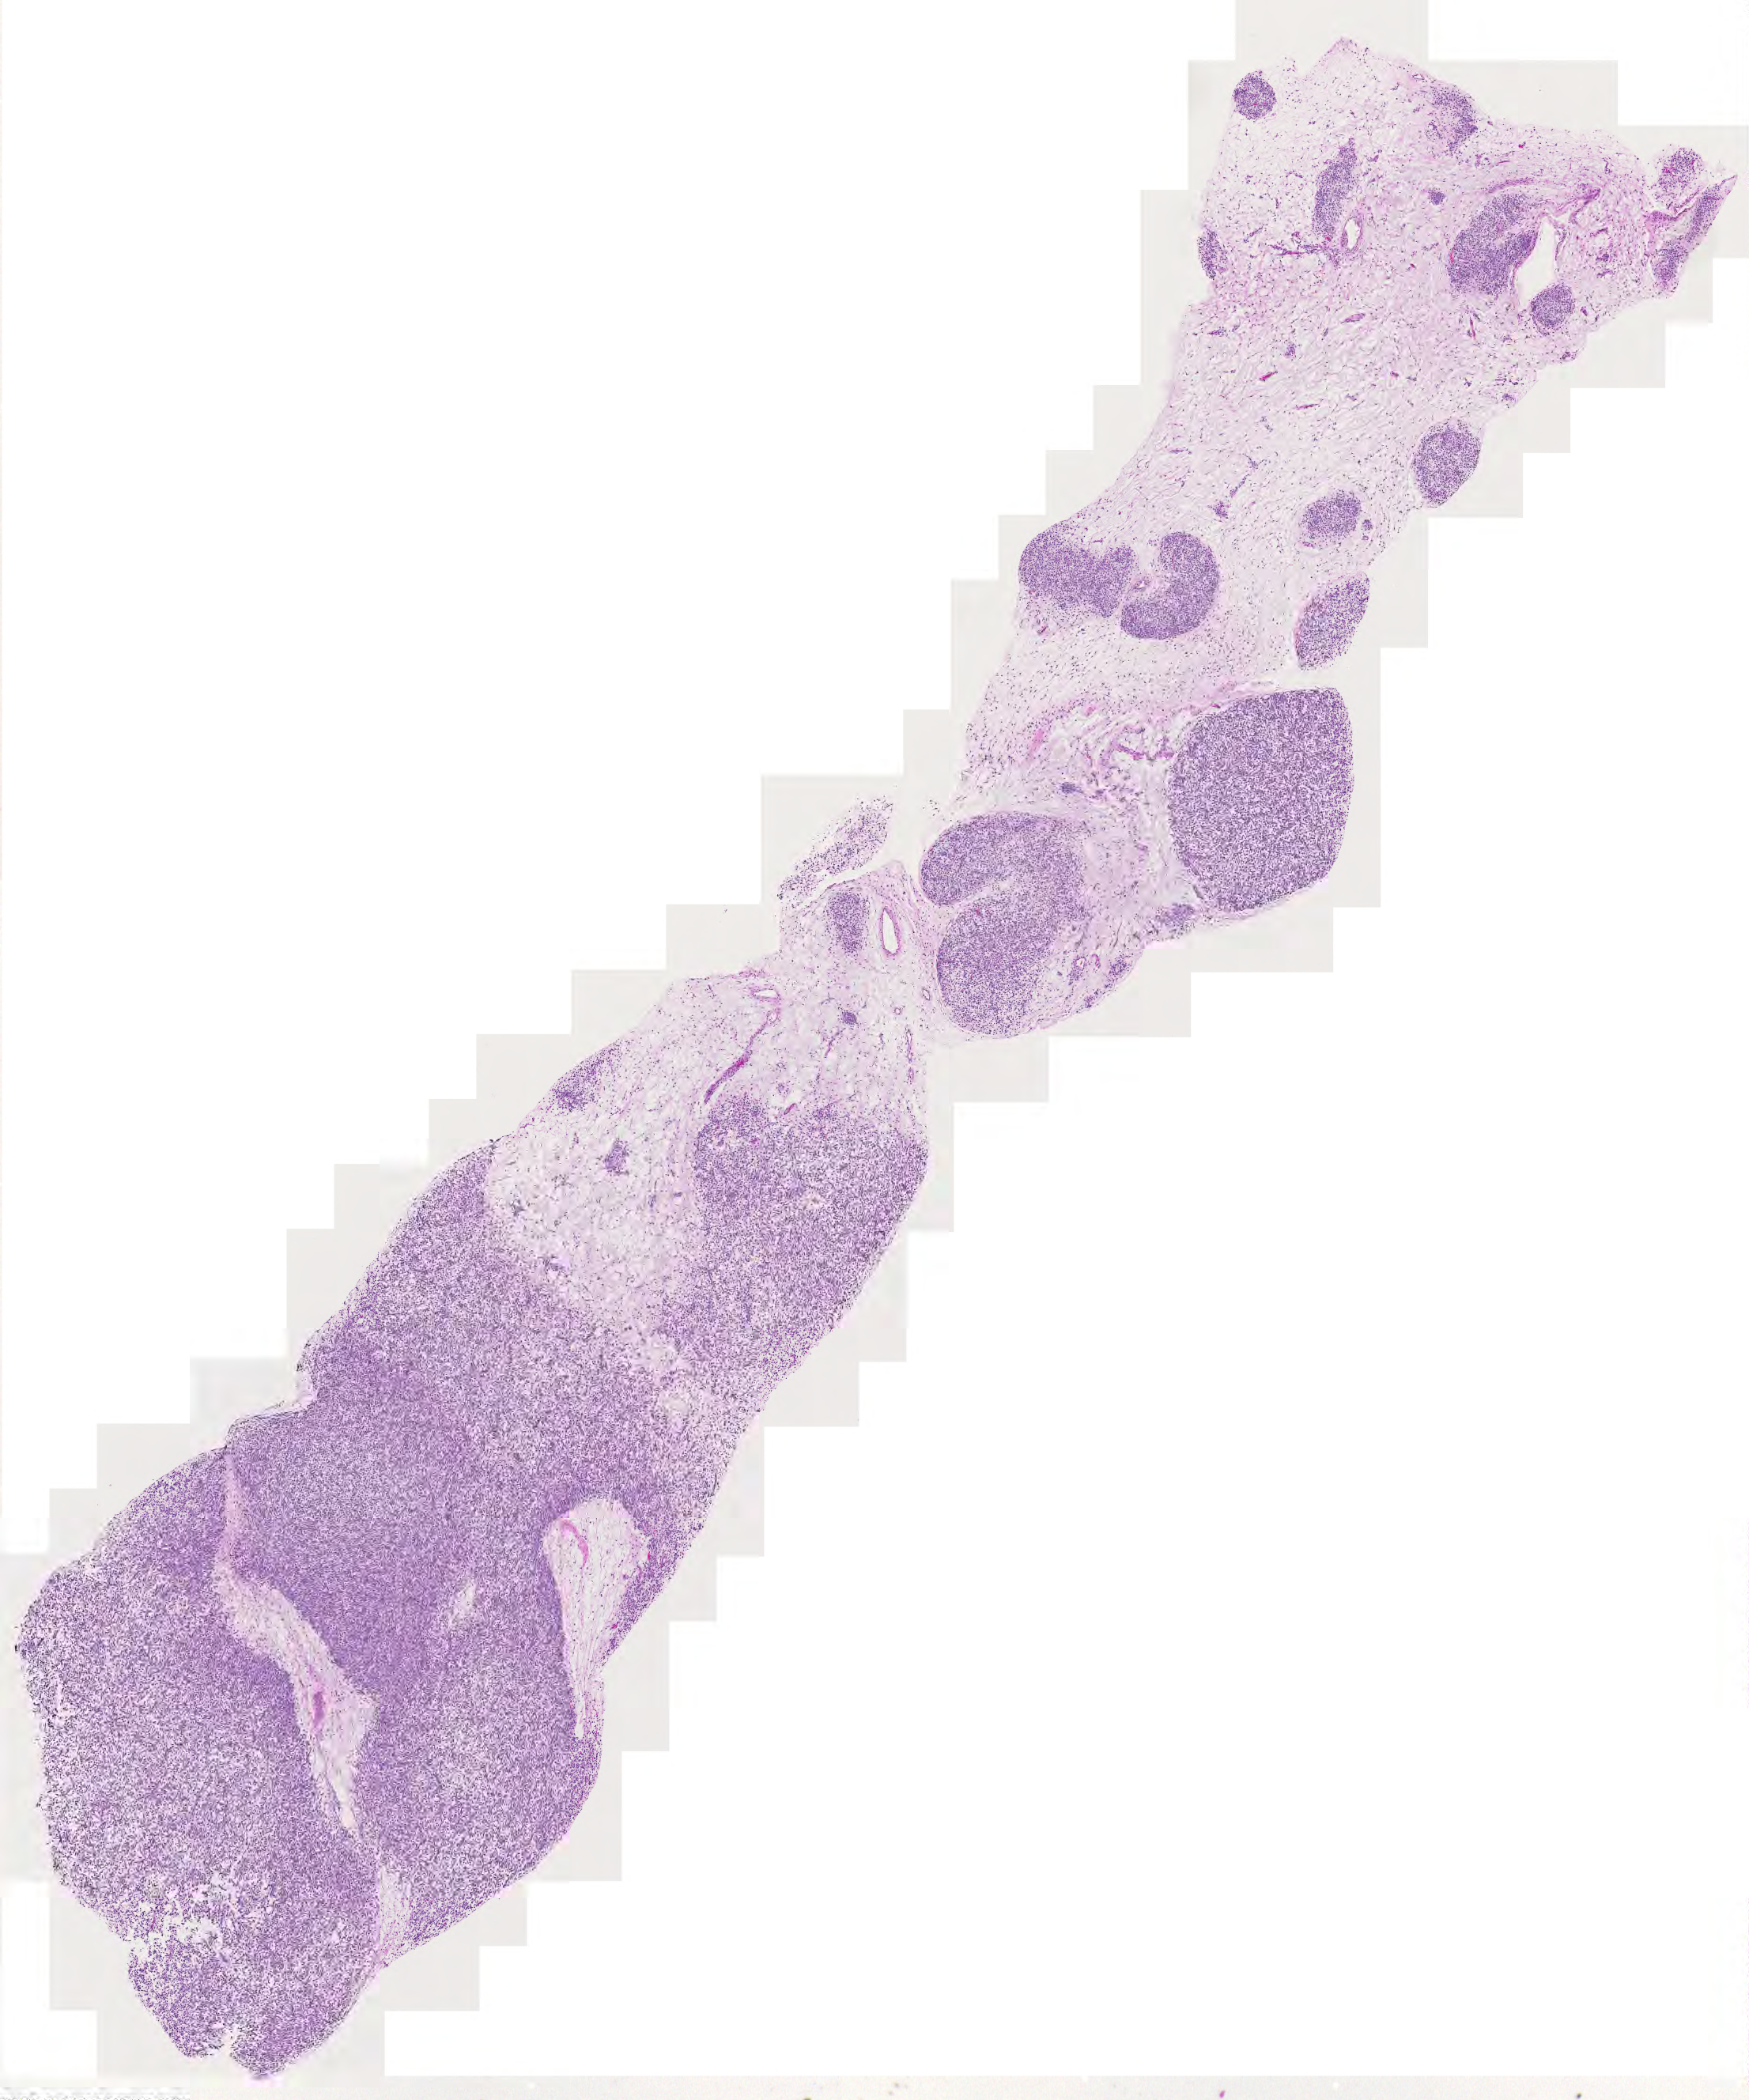
H&E-stained whole-slide image, shown as a low-resolution overview of the whole scanned area (about 11.4 x 13.7 mm, from a 20x scan), tumour tissue sample. Female, 41 y/o.
Primary tumour site (as recorded): lower extremity. Patient diagnosis (cohort enrolment): sarcoma (site not recorded at cohort level).